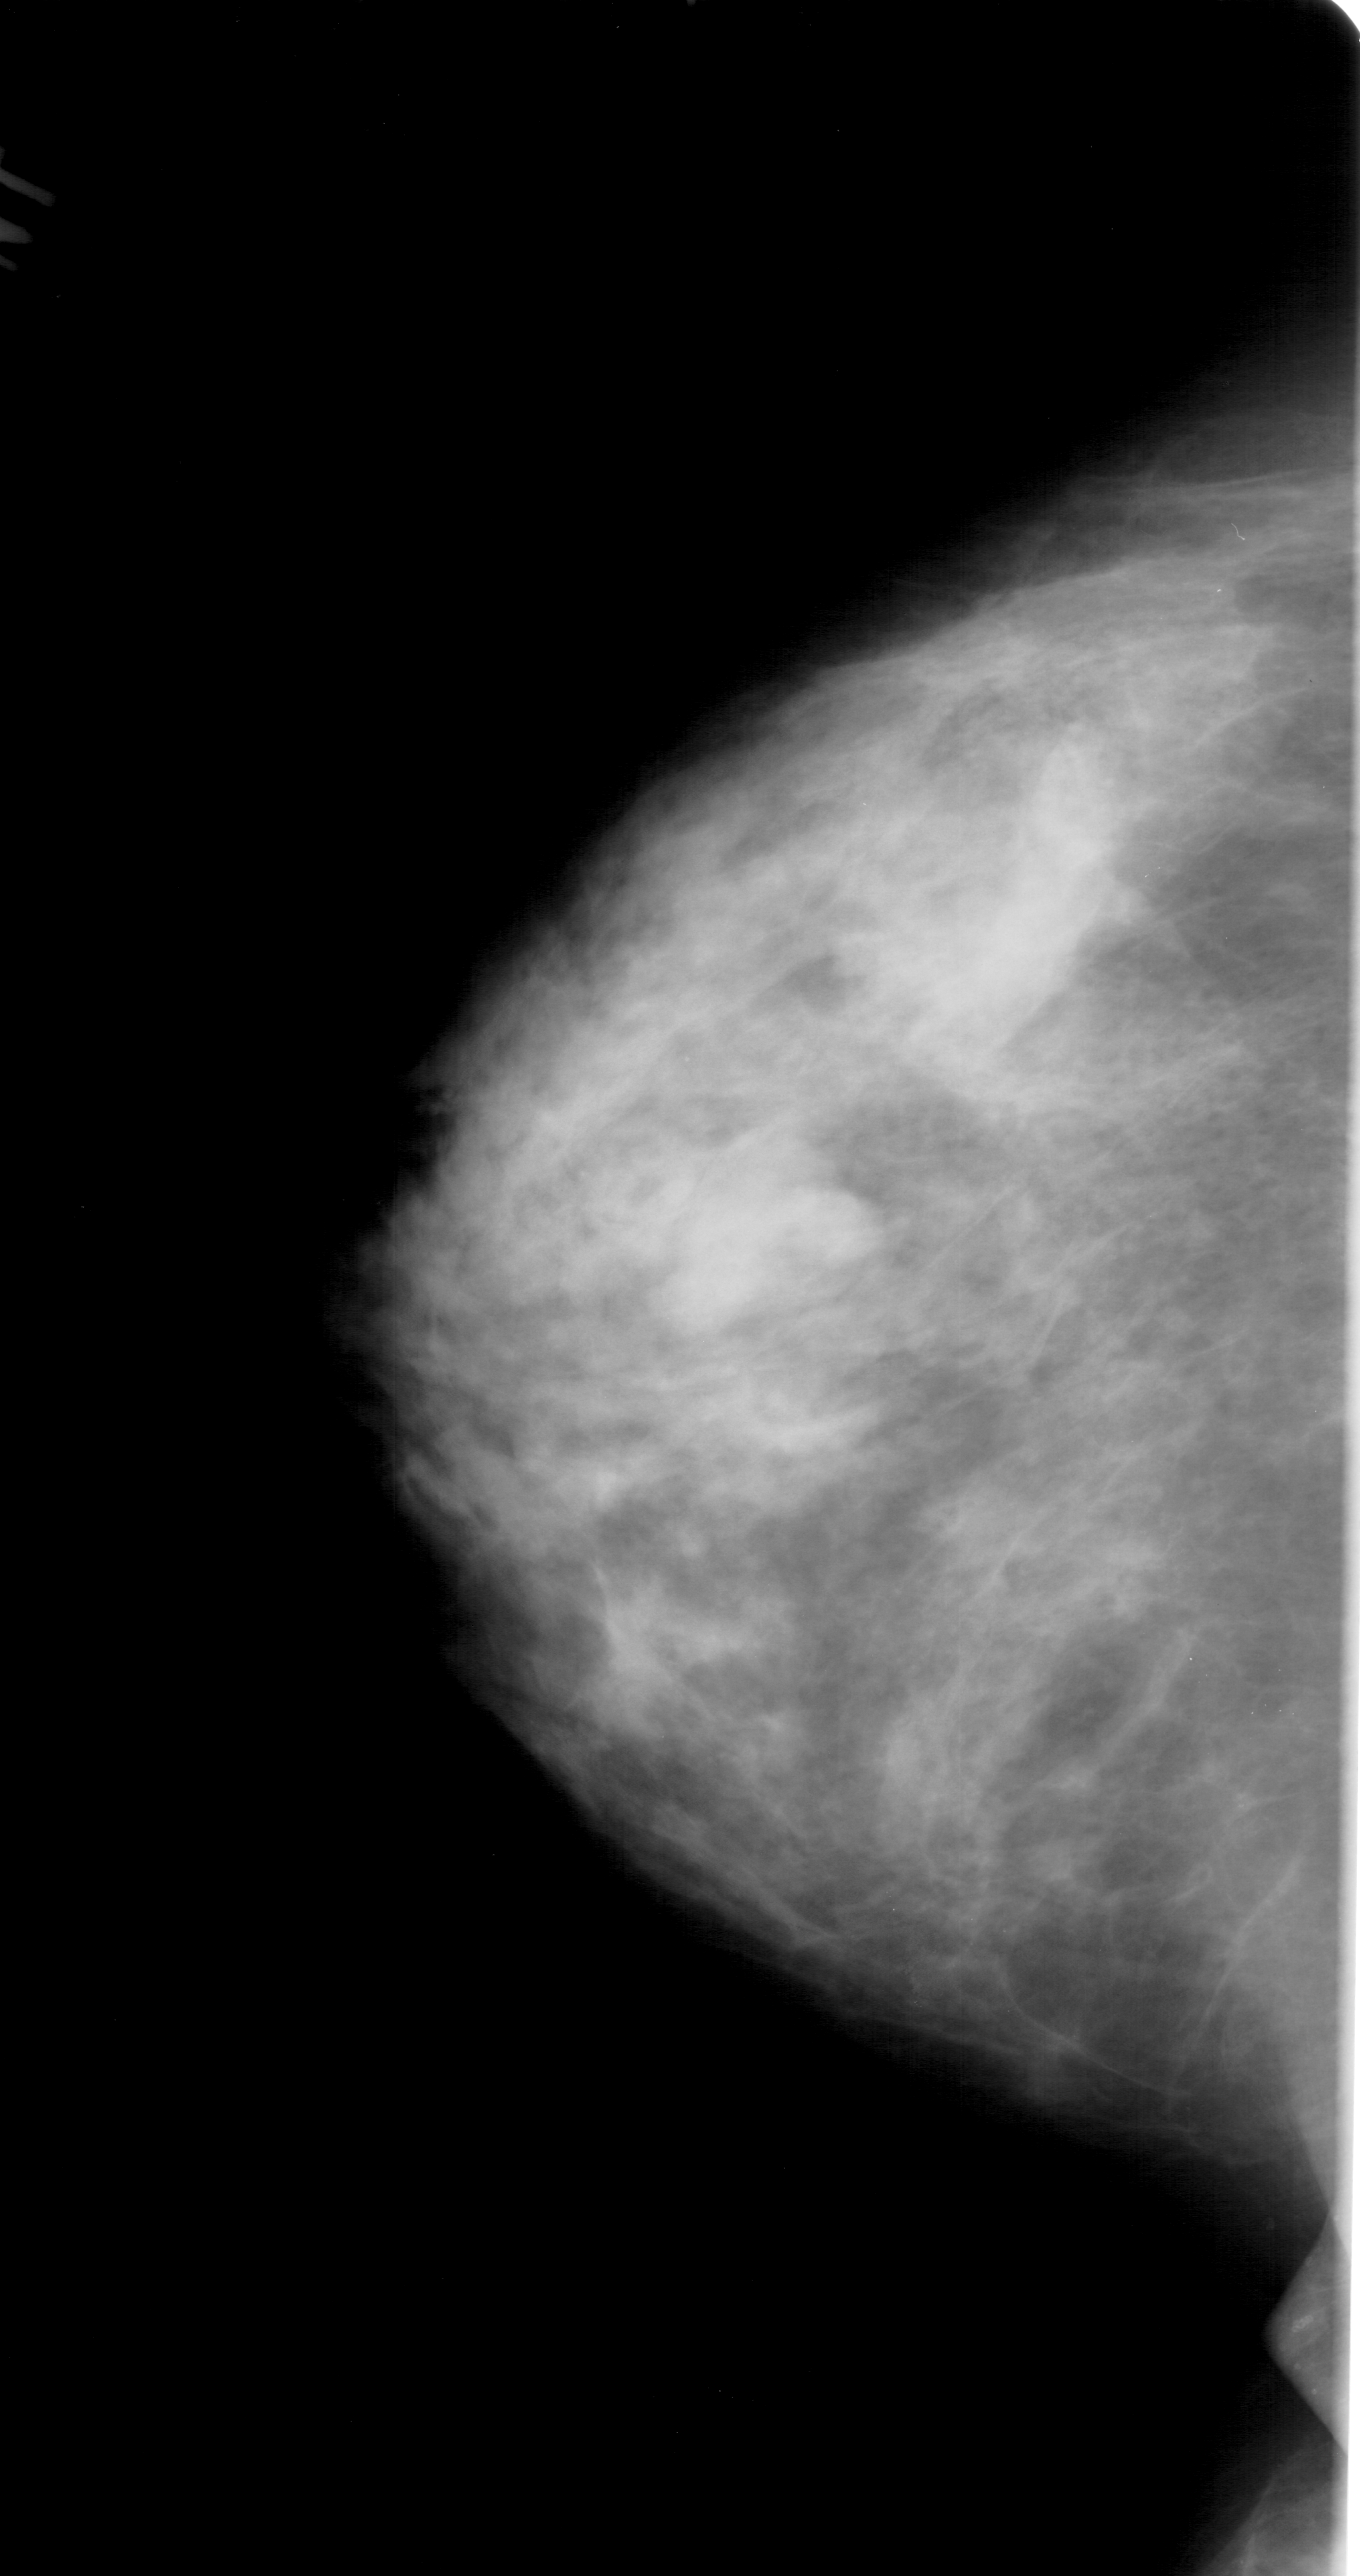
Digitized screen-film mammogram; left breast; craniocaudal (CC) view; BI-RADS breast density category 3 (scale 1–4); 1360 × 2576 image matrix.
Expert-marked regions of interest on this film, with their recorded descriptors:
- mass, shape lobulated, margins obscured; BI-RADS assessment category 4; subtlety rating 2 on a 1 (subtle) to 5 (obvious) scale; pathology result (as recorded, not read from the image): benign: bounding box <678,1165,853,1304> (left, top, right, bottom; pixels)